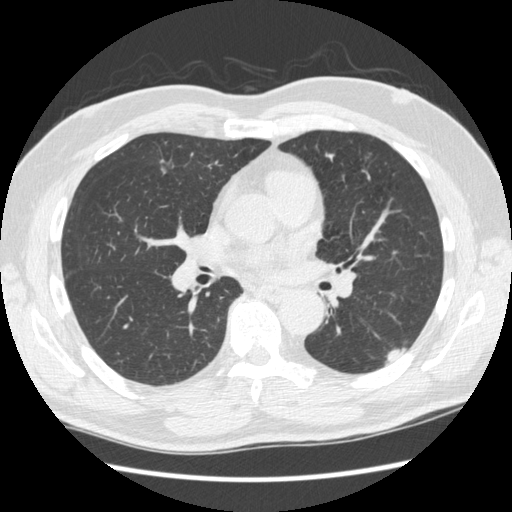
Chest CT (low-dose screening protocol), one axial image, baseline screening round, lung window (W 1500 / L -600 HU), standard (soft-tissue) reconstruction kernel (STANDARD), 120 kVp, slice 122 of 267 in the series. Male participant, aged 74 years at enrolment. Former smoker at enrolment.
Expert-annotated lung lesion, bounding box (x1, y1, x2, y2) in pixels: (373, 324, 415, 369). The screening reader recorded 3 non-calcified nodules or masses ≥4 mm on this exam; which of them this box marks is not recorded. Official screen result: positive, change unspecified: nodule(s) >= 4 mm or enlarging nodule(s), mass(es), or other non-specific abnormalities suspicious for lung cancer. Participant outcome: lung cancer diagnosed 384 days after this screen — squamous cell carcinoma, NOS, left lower lobe, well differentiated (G1), stage IA (AJCC 6th edition), 28 mm at pathology.